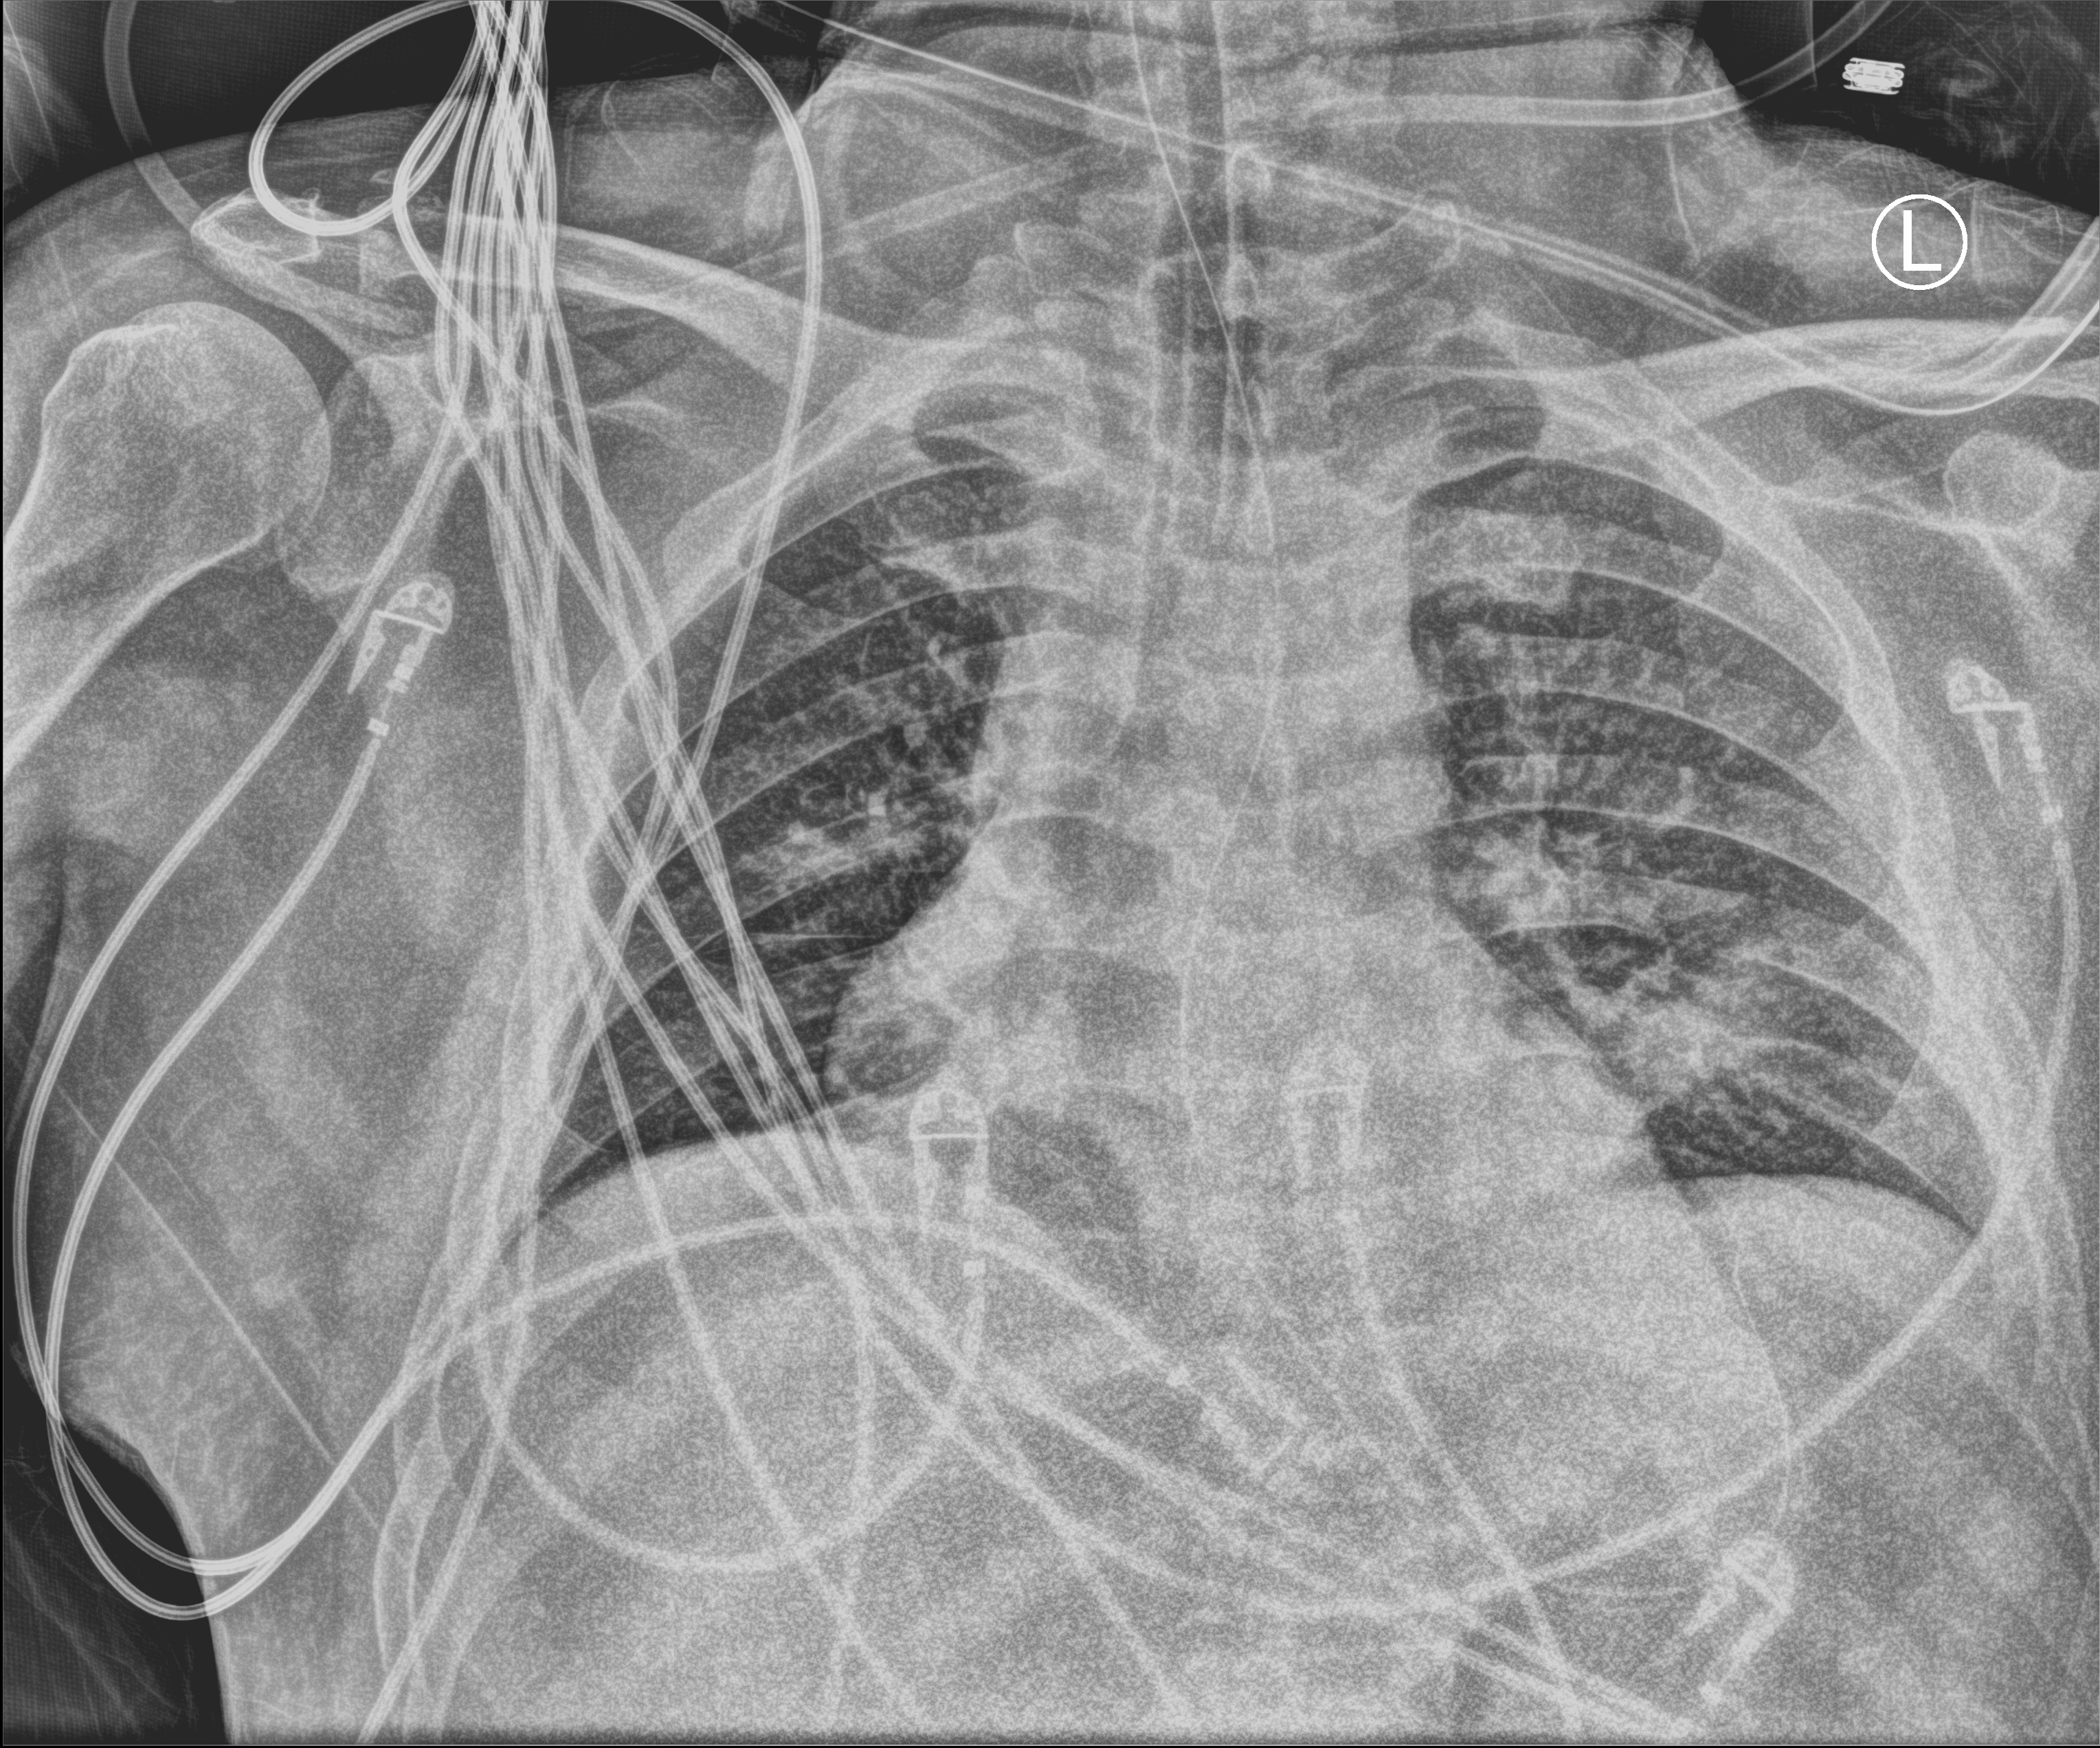
Chest X-ray (portable); anteroposterior (AP) projection. Male patient hospitalised with COVID-19, age 18–59 years.
Hospital-stay facts (about this admission, not read from this image; timing relative to this image not recorded):
- mechanically ventilated during this hospital stay: yes
- length of hospital stay: 65 days